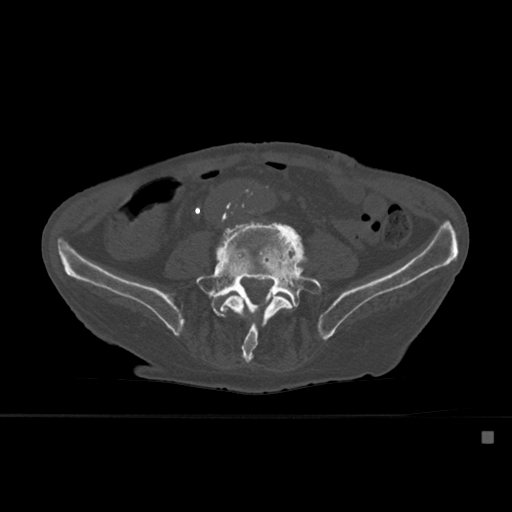
CT including the spine, one axial slice; position 183 of 527 along the scan axis; bone window (W 1800 / L 400 HU); 512 × 512 image matrix, field of view 373 × 373 mm. Male patient, age 78 years. Case-level facts recorded for this patient, not image findings: primary cancer: prostate.
Structures marked on this image (semi-automatically segmented with operator editing):
- L4 vertebra: bounding box [x1, y1, x2, y2] px = [220, 290, 294, 364]
- L5 vertebra: [195, 227, 323, 325]